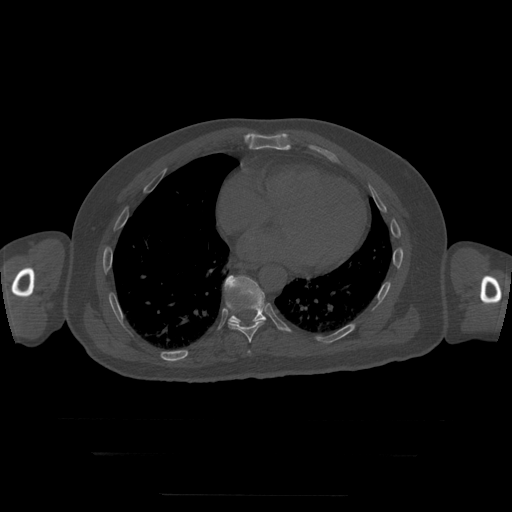
CT including the spine, one axial slice; position 137 of 397 along the scan axis; reconstruction kernel STANDARD; 120 kVp; bone window (W 1800 / L 400 HU); 1.25 mm slice thickness; 512 × 512 image matrix, field of view 510 × 510 mm. Patient age 73 years. From the clinical record (not read from this slice): primary cancer: prostate.
Annotated regions visible in this slice (semi-automatically segmented with operator editing):
- T10 vertebra: bounding box <225,276,266,324> (left, top, right, bottom; pixels)
- T8 vertebra: <248,351,251,353>
- T9 vertebra: <226,302,266,343>